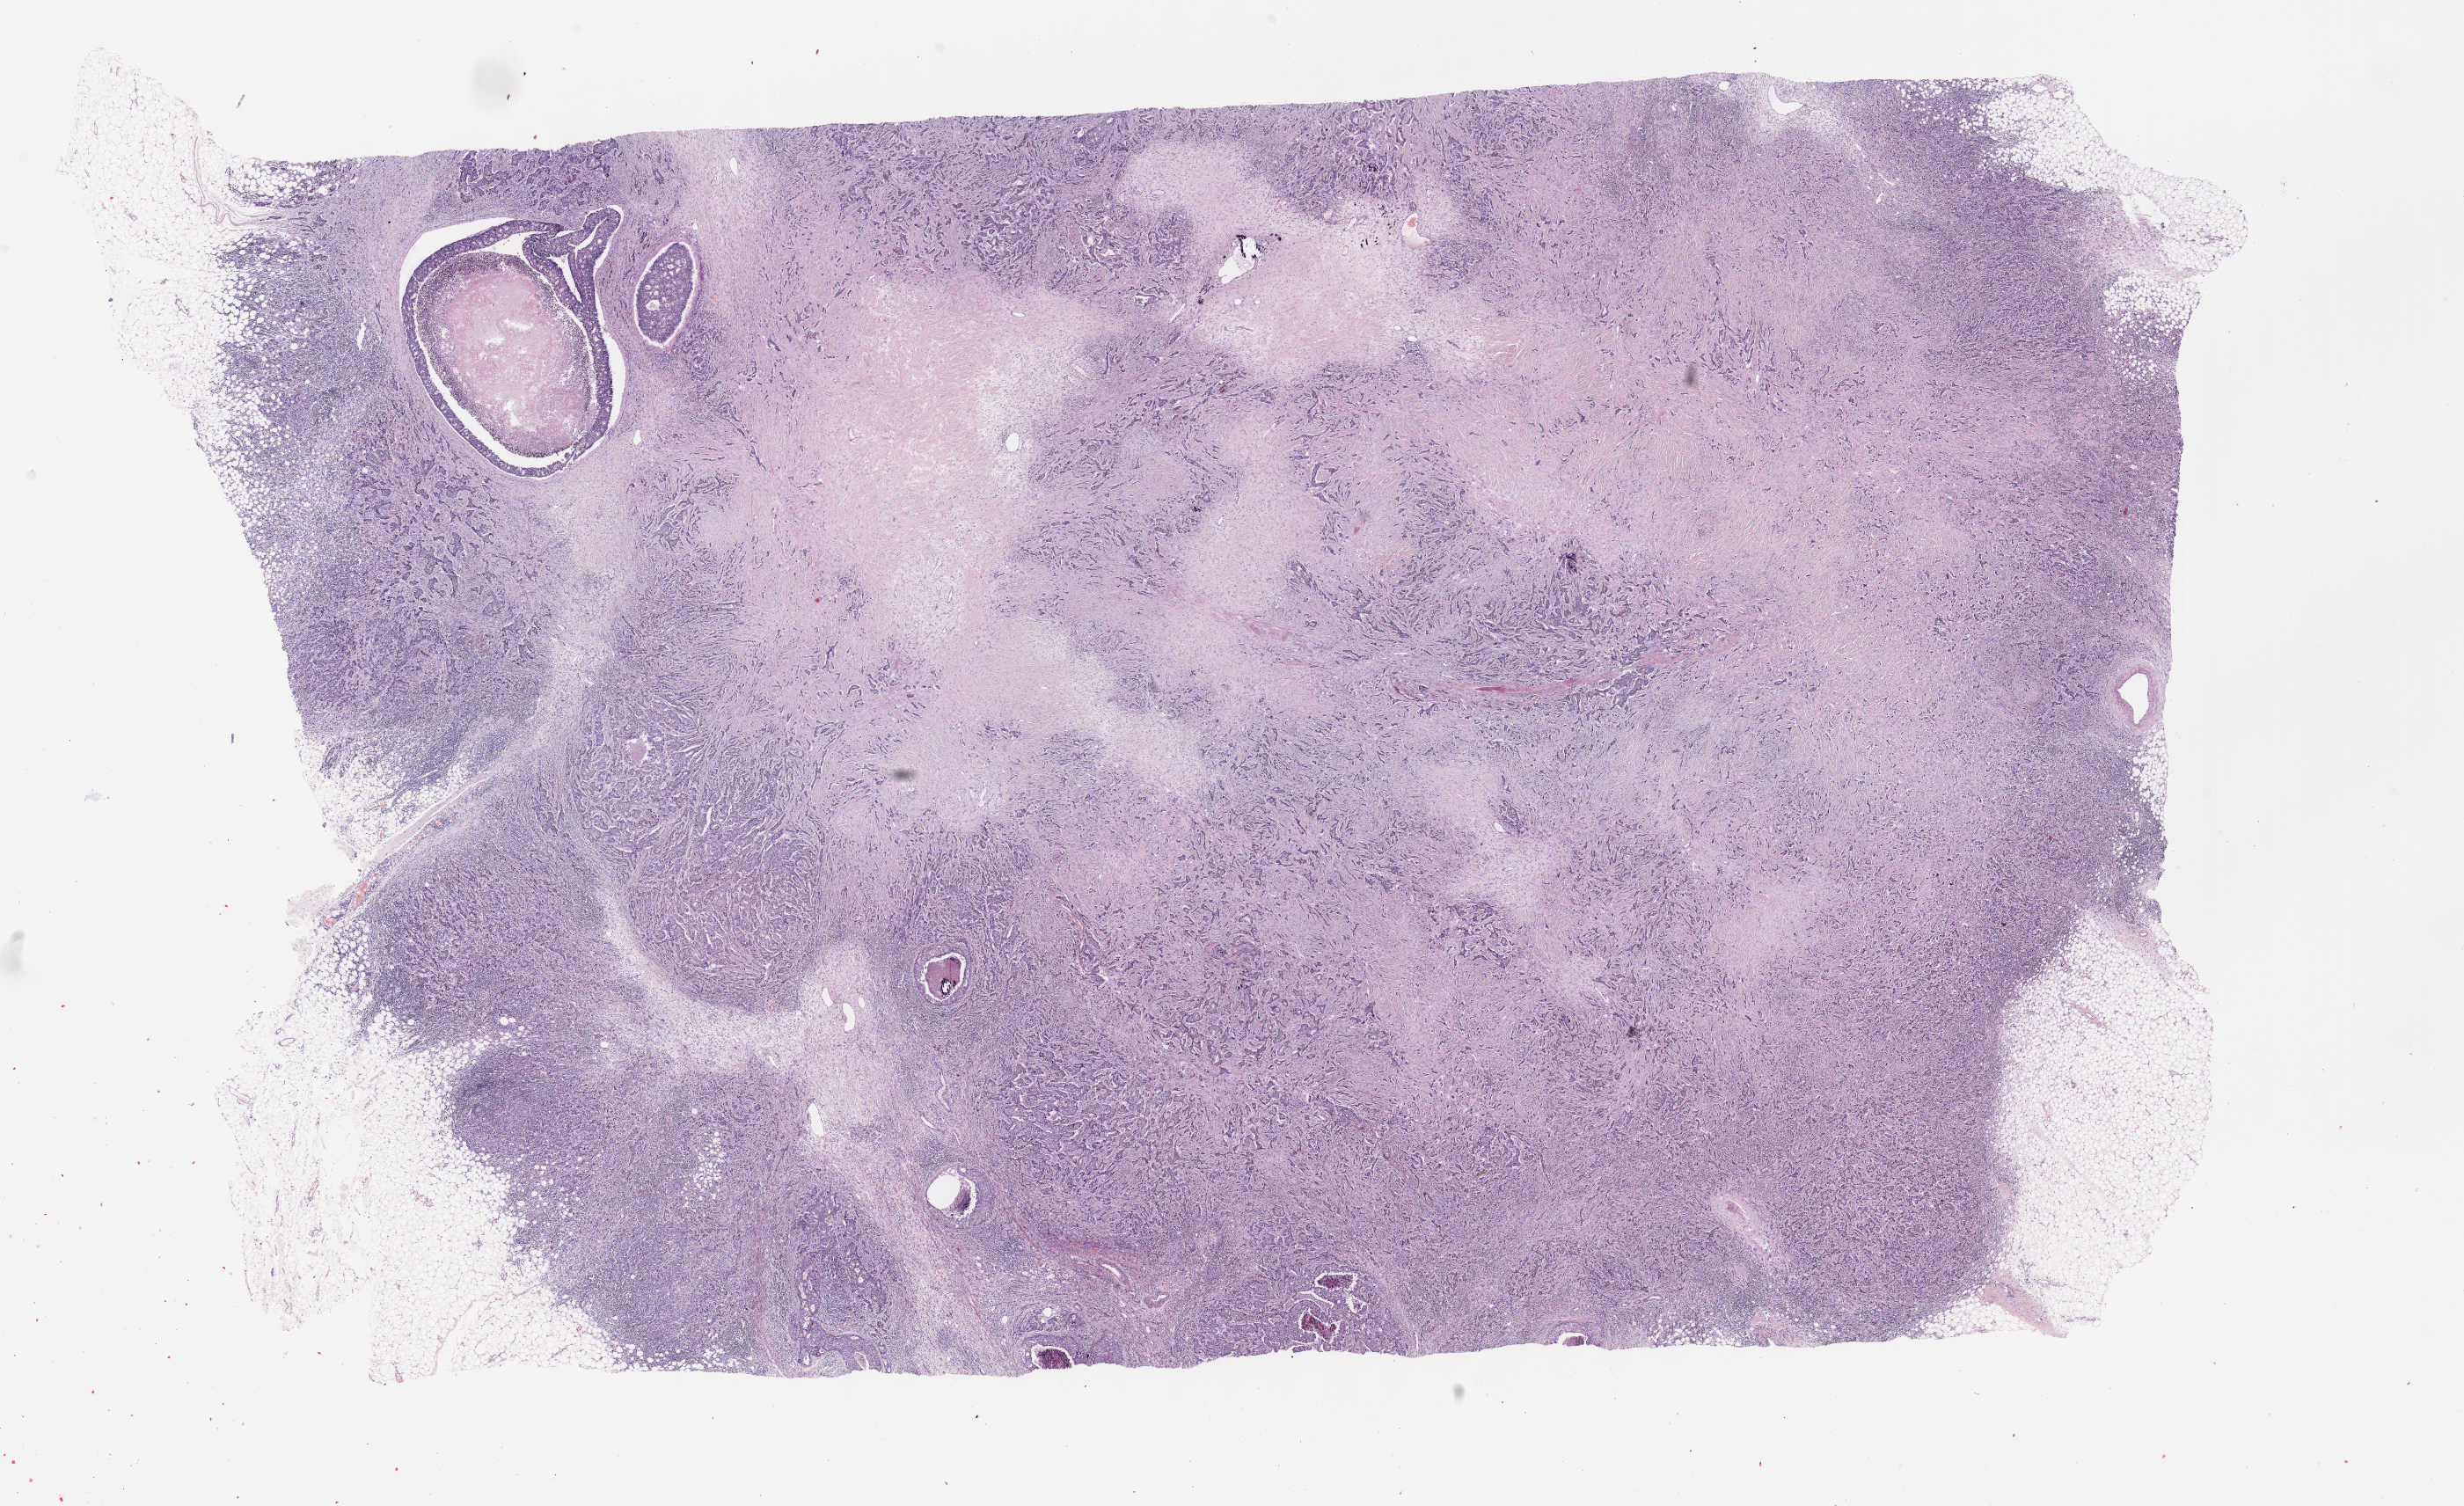
Whole-slide histology image, H&E, a low-resolution overview of the entire scanned area, about 22.7 x 13.8 mm; formalin-fixed paraffin-embedded (FFPE) diagnostic section; breast, primary tumour sample. Female patient; age at initial diagnosis 41 years.
• AJCC pathologic stage: IIB (7th edition)
• diagnosis: Infiltrating duct carcinoma, NOS
• TNM: T2 N1a M0